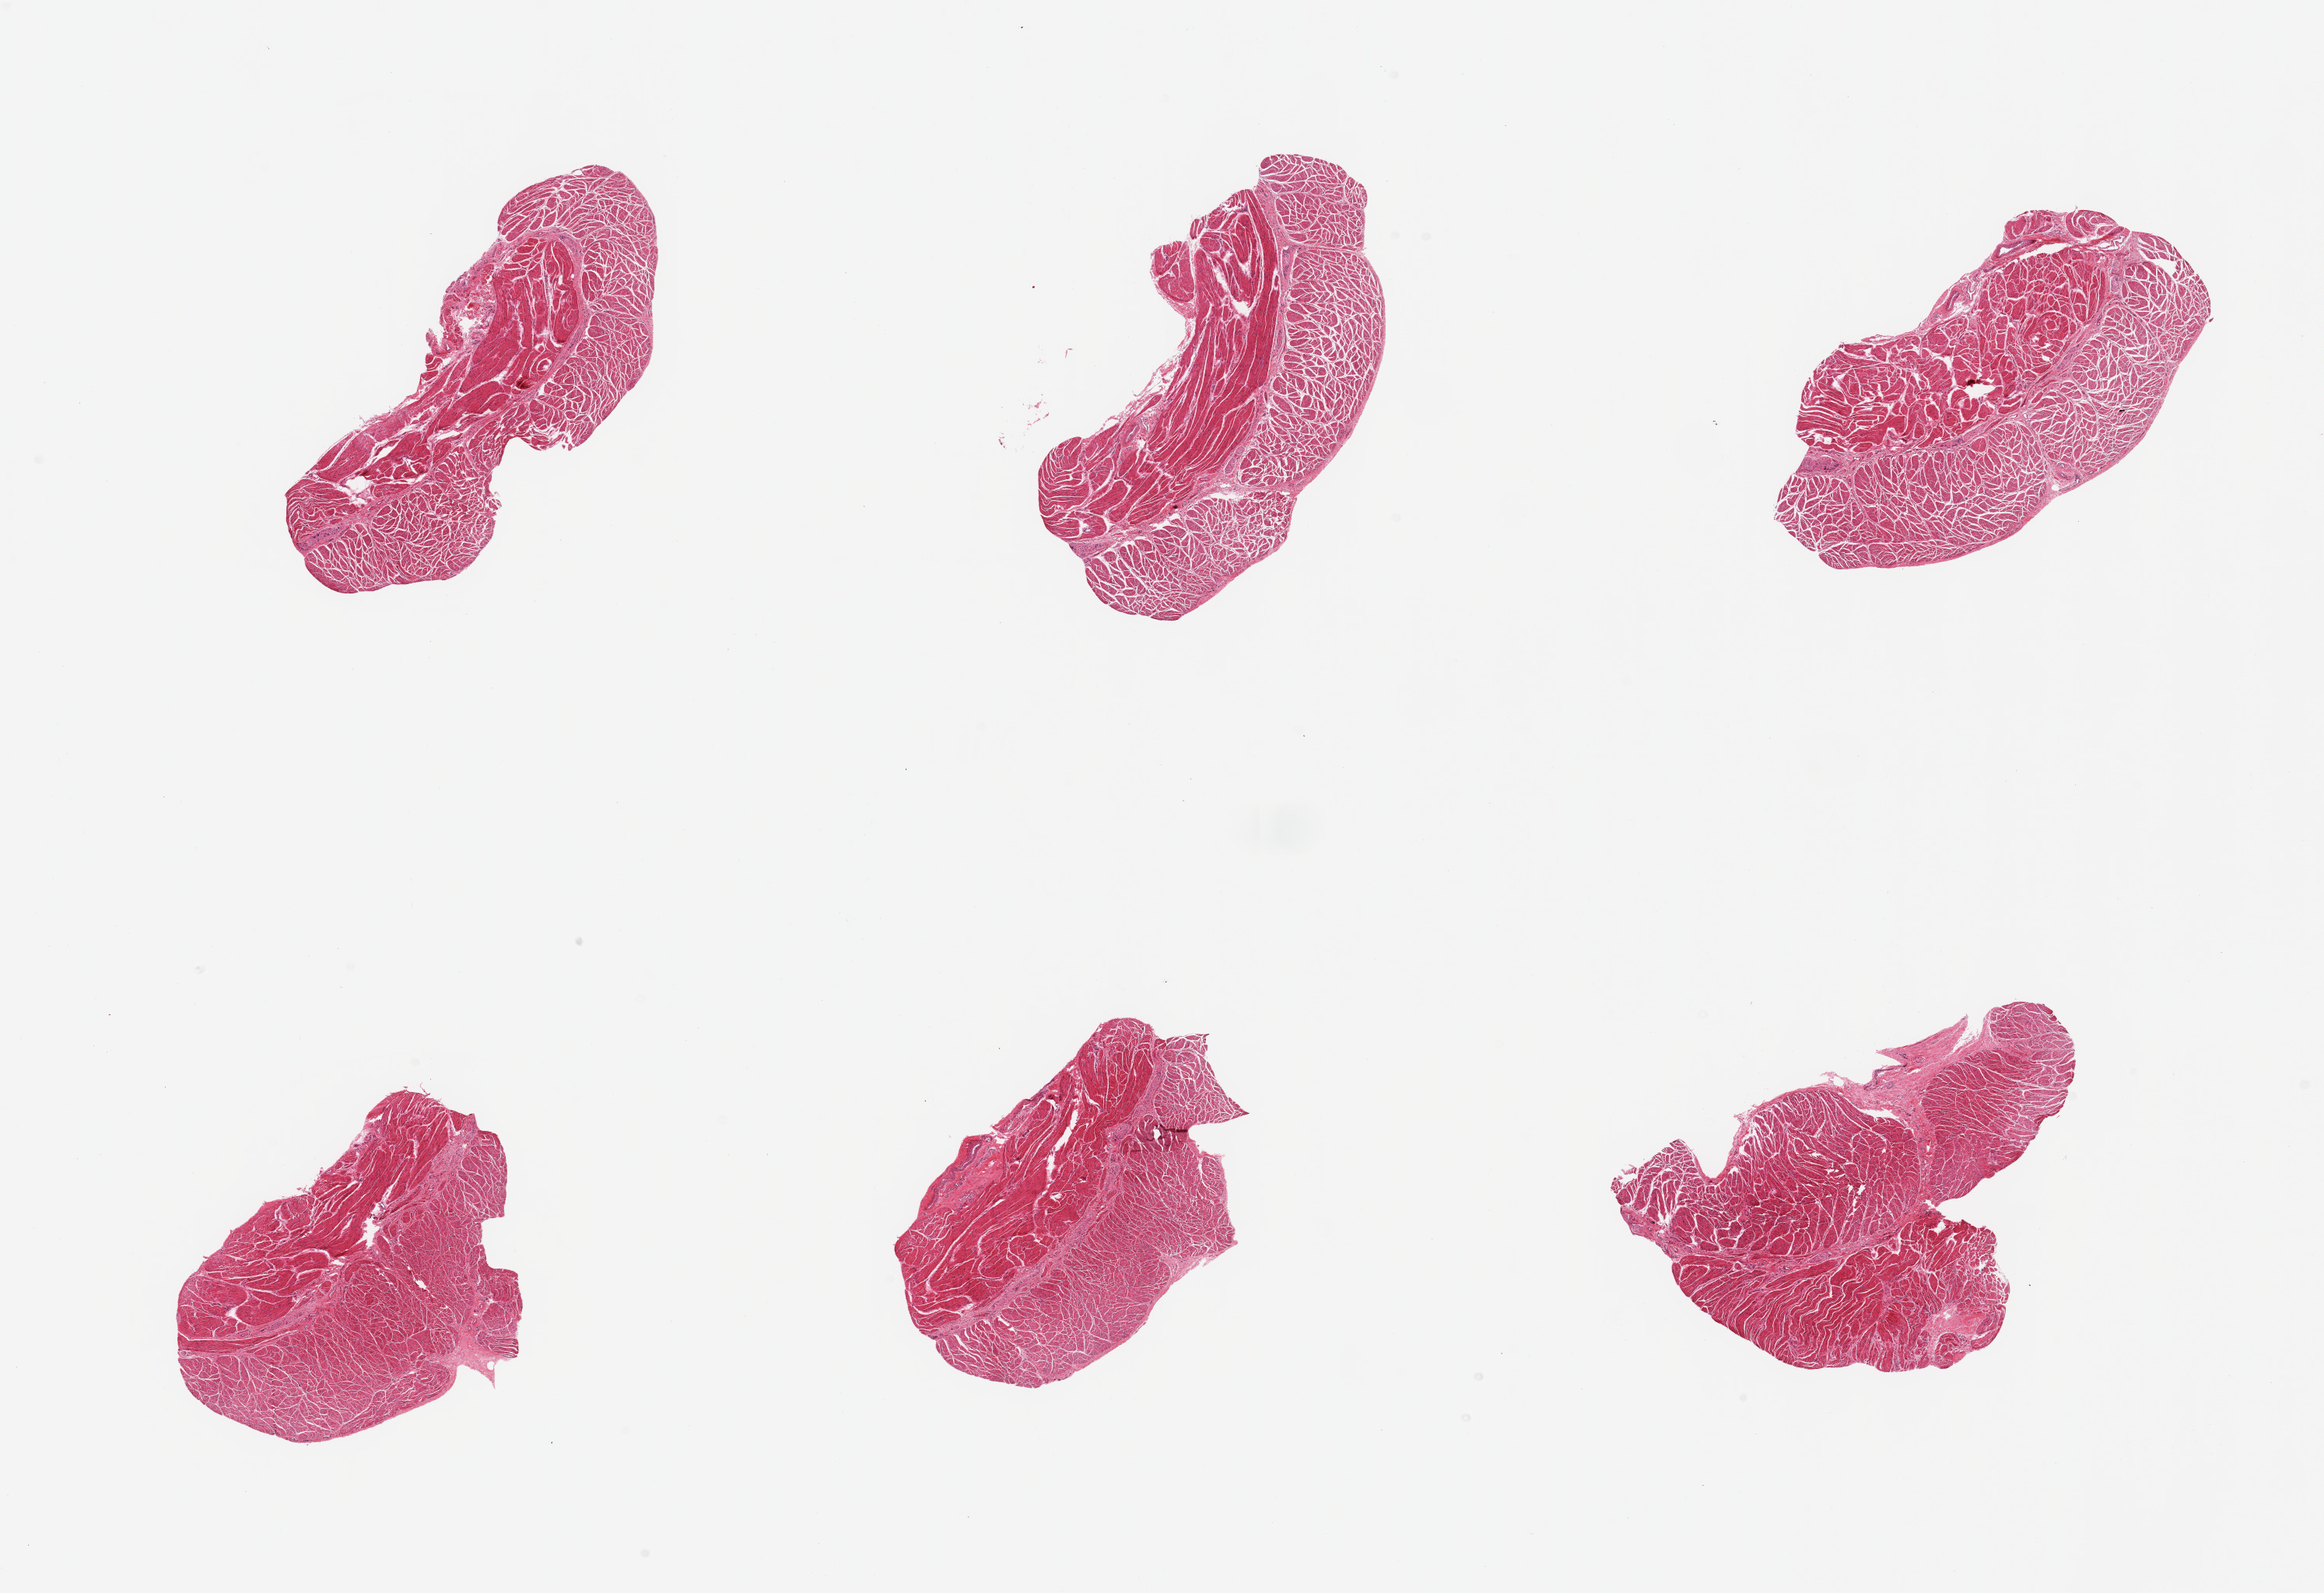
Hematoxylin and eosin (H&E) whole-slide image, a low-resolution overview of the entire scanned area, about 23.6 x 16.2 mm; PAXgene-fixed paraffin-embedded (PFPE) section; section of esophageal muscle (target tissue); tissue donor sample.
• reviewer comment on this tissue sample: 6 pieces; target muscularis